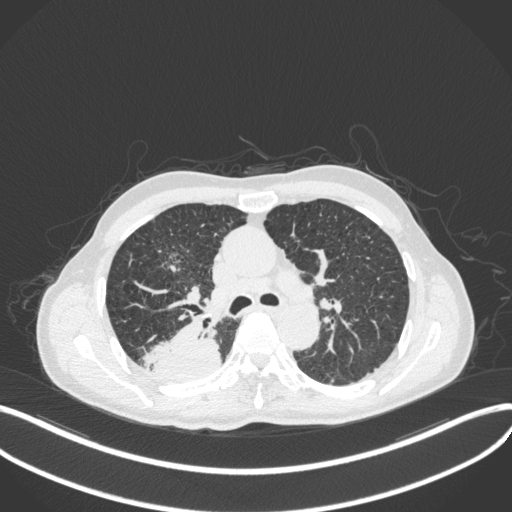
Chest CT, one axial slice; position 296 of 423 along the scan axis; 120 kVp; lung window (W 1500 / L -600 HU); 512 × 512 image matrix. Patient: male, 79 years. From the clinical record (not read from this slice): clinical TNM (as recorded): T3 N0 M0.
Structures marked on this image (bounding box drawn by a radiologist):
- lung tumour (recorded histology: adenocarcinoma): bounding box (x1, y1, x2, y2) in pixels: (143, 313, 223, 384)